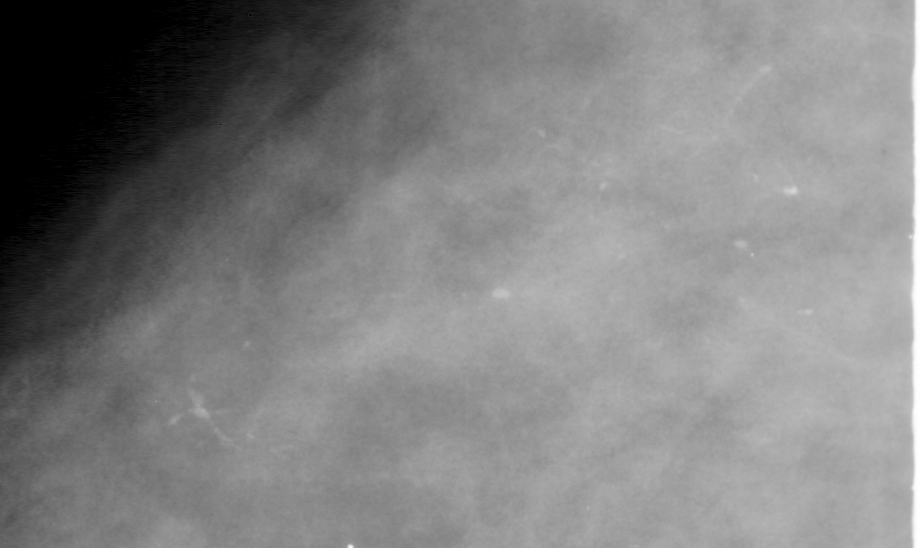
Cropped region of a digitized screen-film mammogram centred on a radiologist-marked abnormality, left breast, CC view, BI-RADS breast density category 4 (scale 1–4).
Calcifications, morphology pleomorphic, distribution segmental; BI-RADS assessment category 4; pathology result (as recorded, not read from the image): malignant.